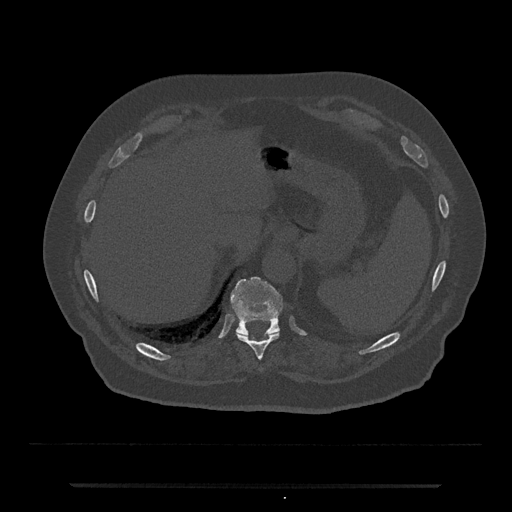
CT including the spine, one axial slice. Position 682 of 797 along the scan axis. Reconstruction kernel Br40s/3. 120 kVp. Bone window (W 1800 / L 400 HU). 0.5 mm slice thickness. 512 × 512 image matrix, field of view 434 × 434 mm. Patient: male, 80 years. From the clinical record (not read from this slice): primary cancer: prostate; vertebrae with lytic lesions (as recorded): L1, T11.
Outlined on this slice (semi-automatic segmentation, software-assisted and operator-edited):
- T10 vertebra: bounding box <236,331,280,360> (left, top, right, bottom; pixels)
- T11 vertebra: <230,276,284,336>